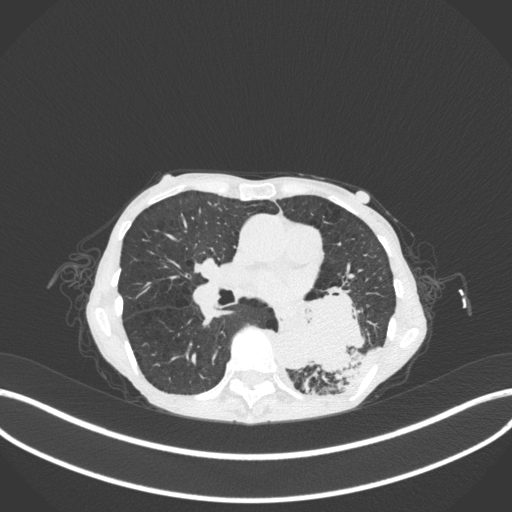
Chest CT, one axial slice. Position 138 of 347 along the scan axis. Lung window (W 1500 / L -600 HU). 1 mm slice thickness. 512 × 512 image matrix. Female patient, age 70 years. From the clinical record (not read from this slice): clinical TNM (as recorded): T3 N0 M0; histopathological grade: G3.
Annotated regions visible in this slice (bounding box drawn by a radiologist):
- lung tumour (recorded histology: small cell carcinoma): bounding box (x1, y1, x2, y2) in pixels: (288, 279, 365, 373)